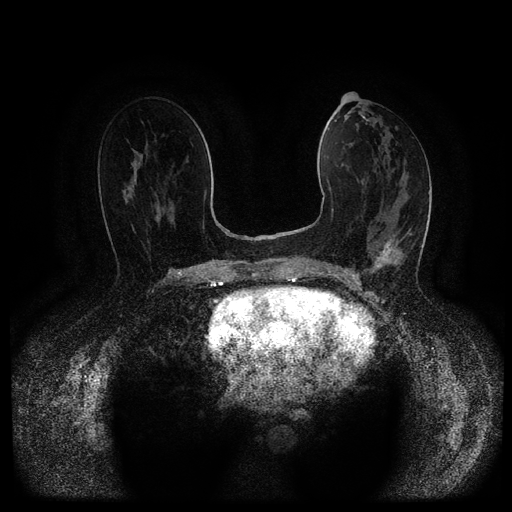
Breast MRI (dynamic contrast-enhanced, multi-phase), one axial slice; slice 52 of 116 in the series (ordered by position); dynamic contrast-enhanced series, time point 2 of 5 at this slice position (early post-contrast); 1.5 T; TE 2.6 ms, TR 5.4 ms; 2 mm slice thickness; 512 × 512 image matrix. Female patient, age 61 years.
Annotated regions visible in this slice (semi-automatically segmented with operator editing):
- breast lesion (labelled 'tumour' in the annotation; benign lesions carry a separate 'benign' label): bounding box [x1, y1, x2, y2] px = [370, 235, 395, 274]